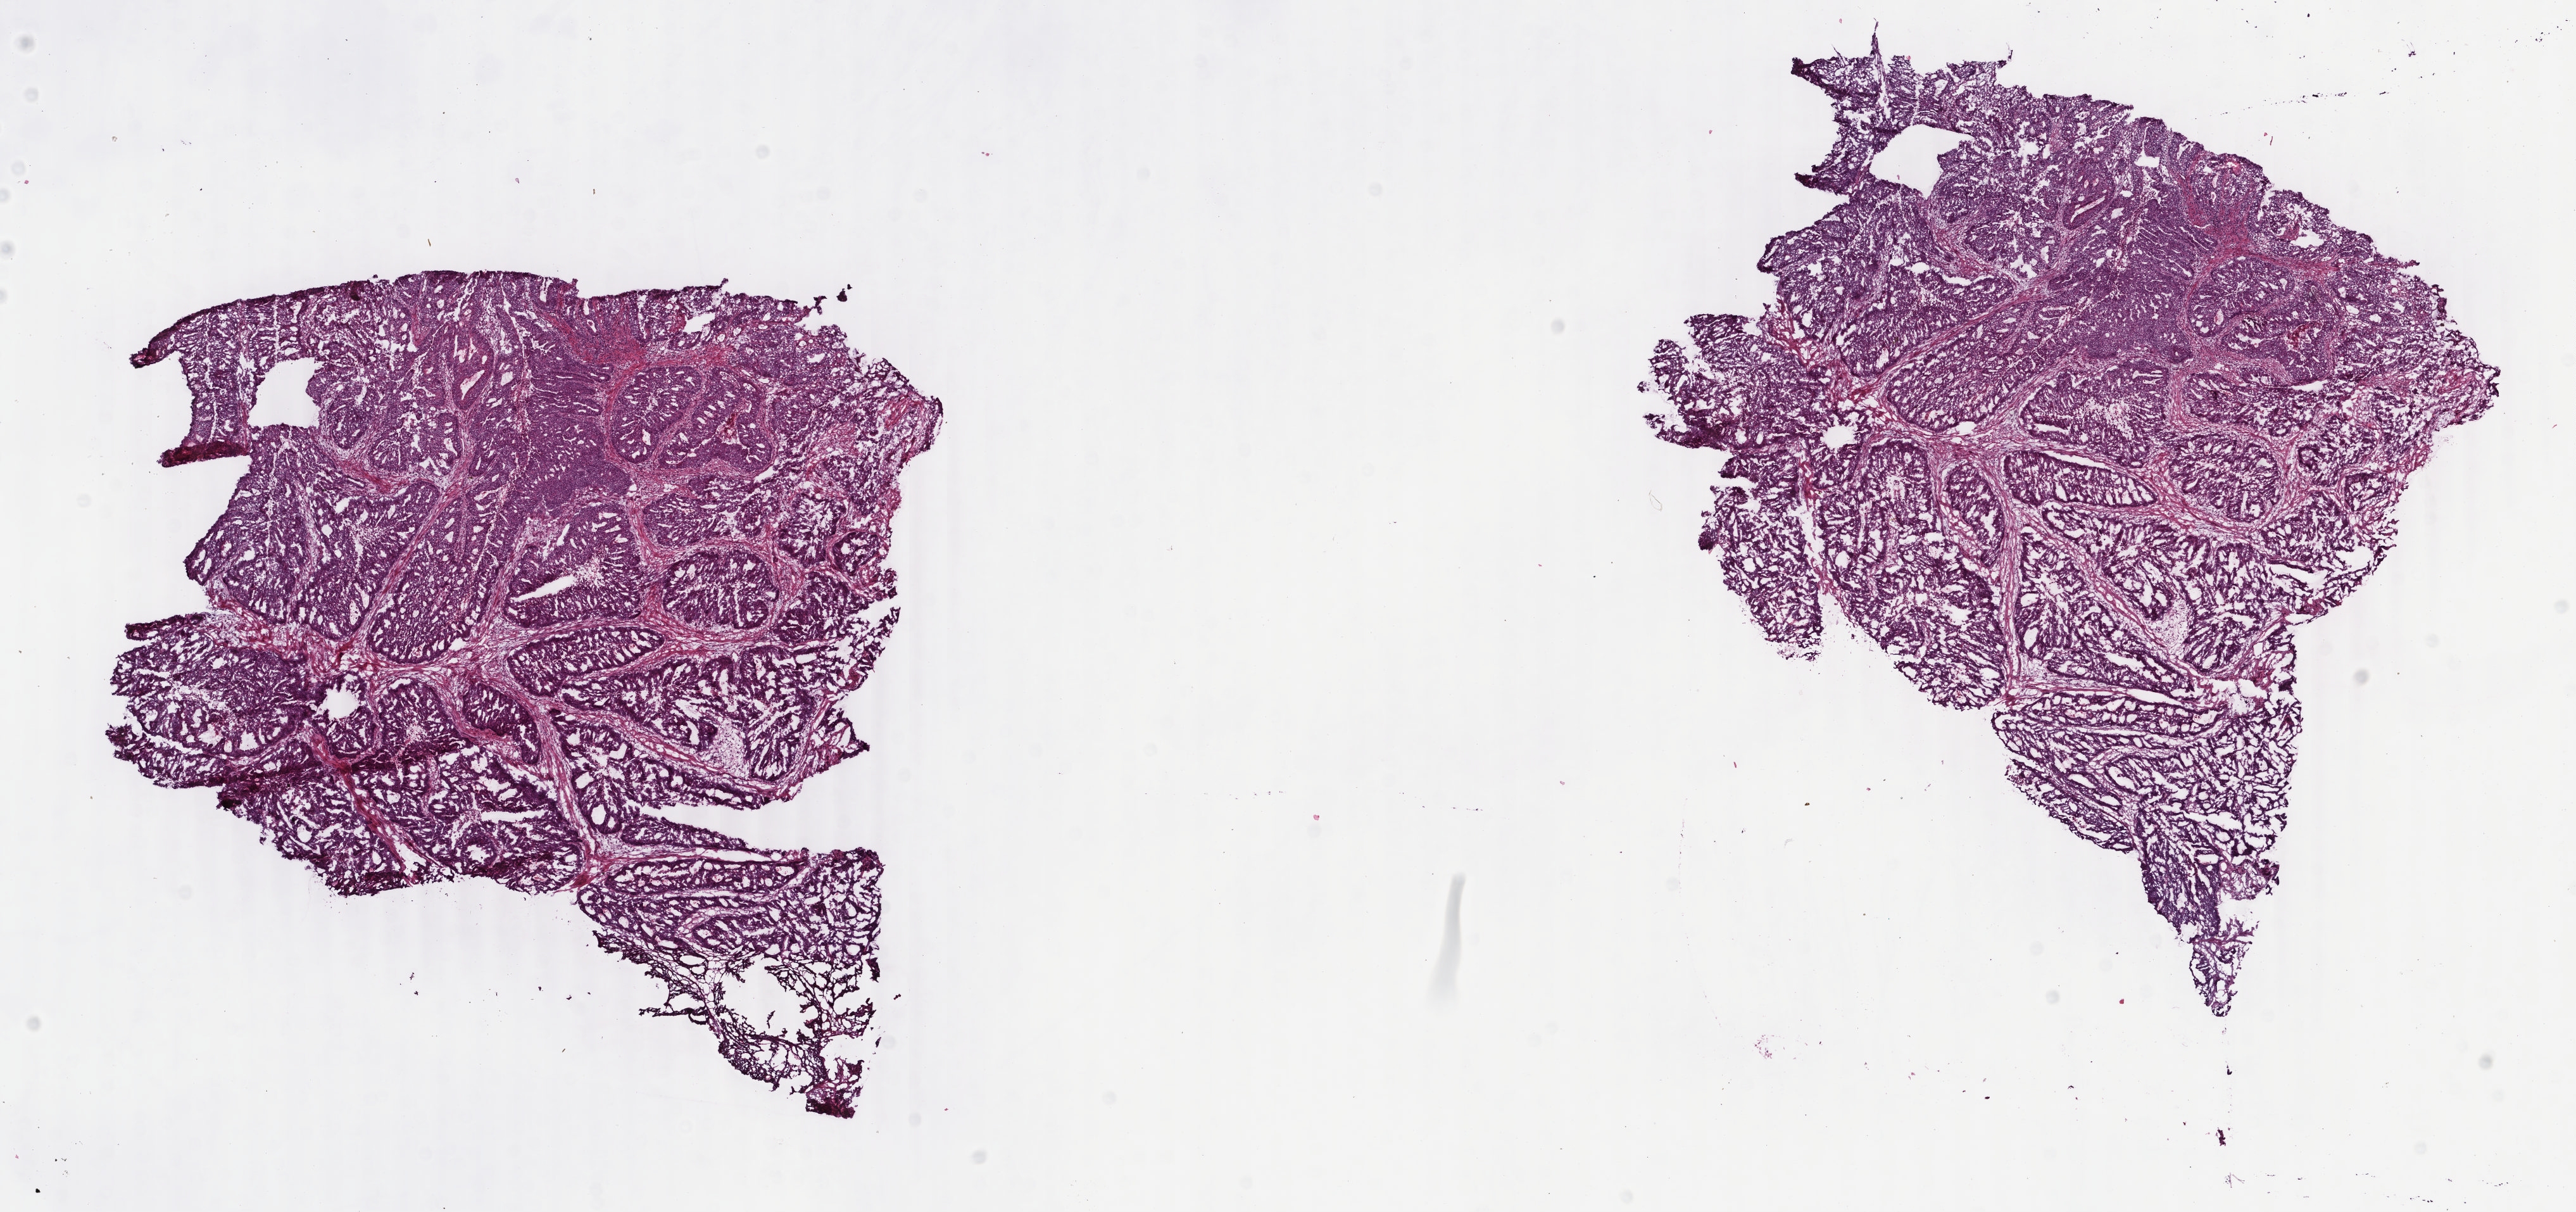
Whole-slide histology image, Hematoxylin and eosin (H&E) stained — whole scanned area (about 16.2 x 7.6 mm) shown as a low-resolution overview; frozen section; primary tumour sample from the colon. Patient: female, age at initial diagnosis 47 years. Pathologist review of this section (percent, as recorded): tumour cells 95%, tumour nuclei 90%, normal cells 0%, stromal cells 4%, necrosis 1%. Inflammatory infiltration, as recorded: lymphocyte infiltration 2%, monocyte infiltration 1%, neutrophil infiltration 2%.
* diagnosis: Adenocarcinoma, NOS (sigmoid colon)
* TNM: T3 N1 M0
* AJCC pathologic stage: III (5th edition)